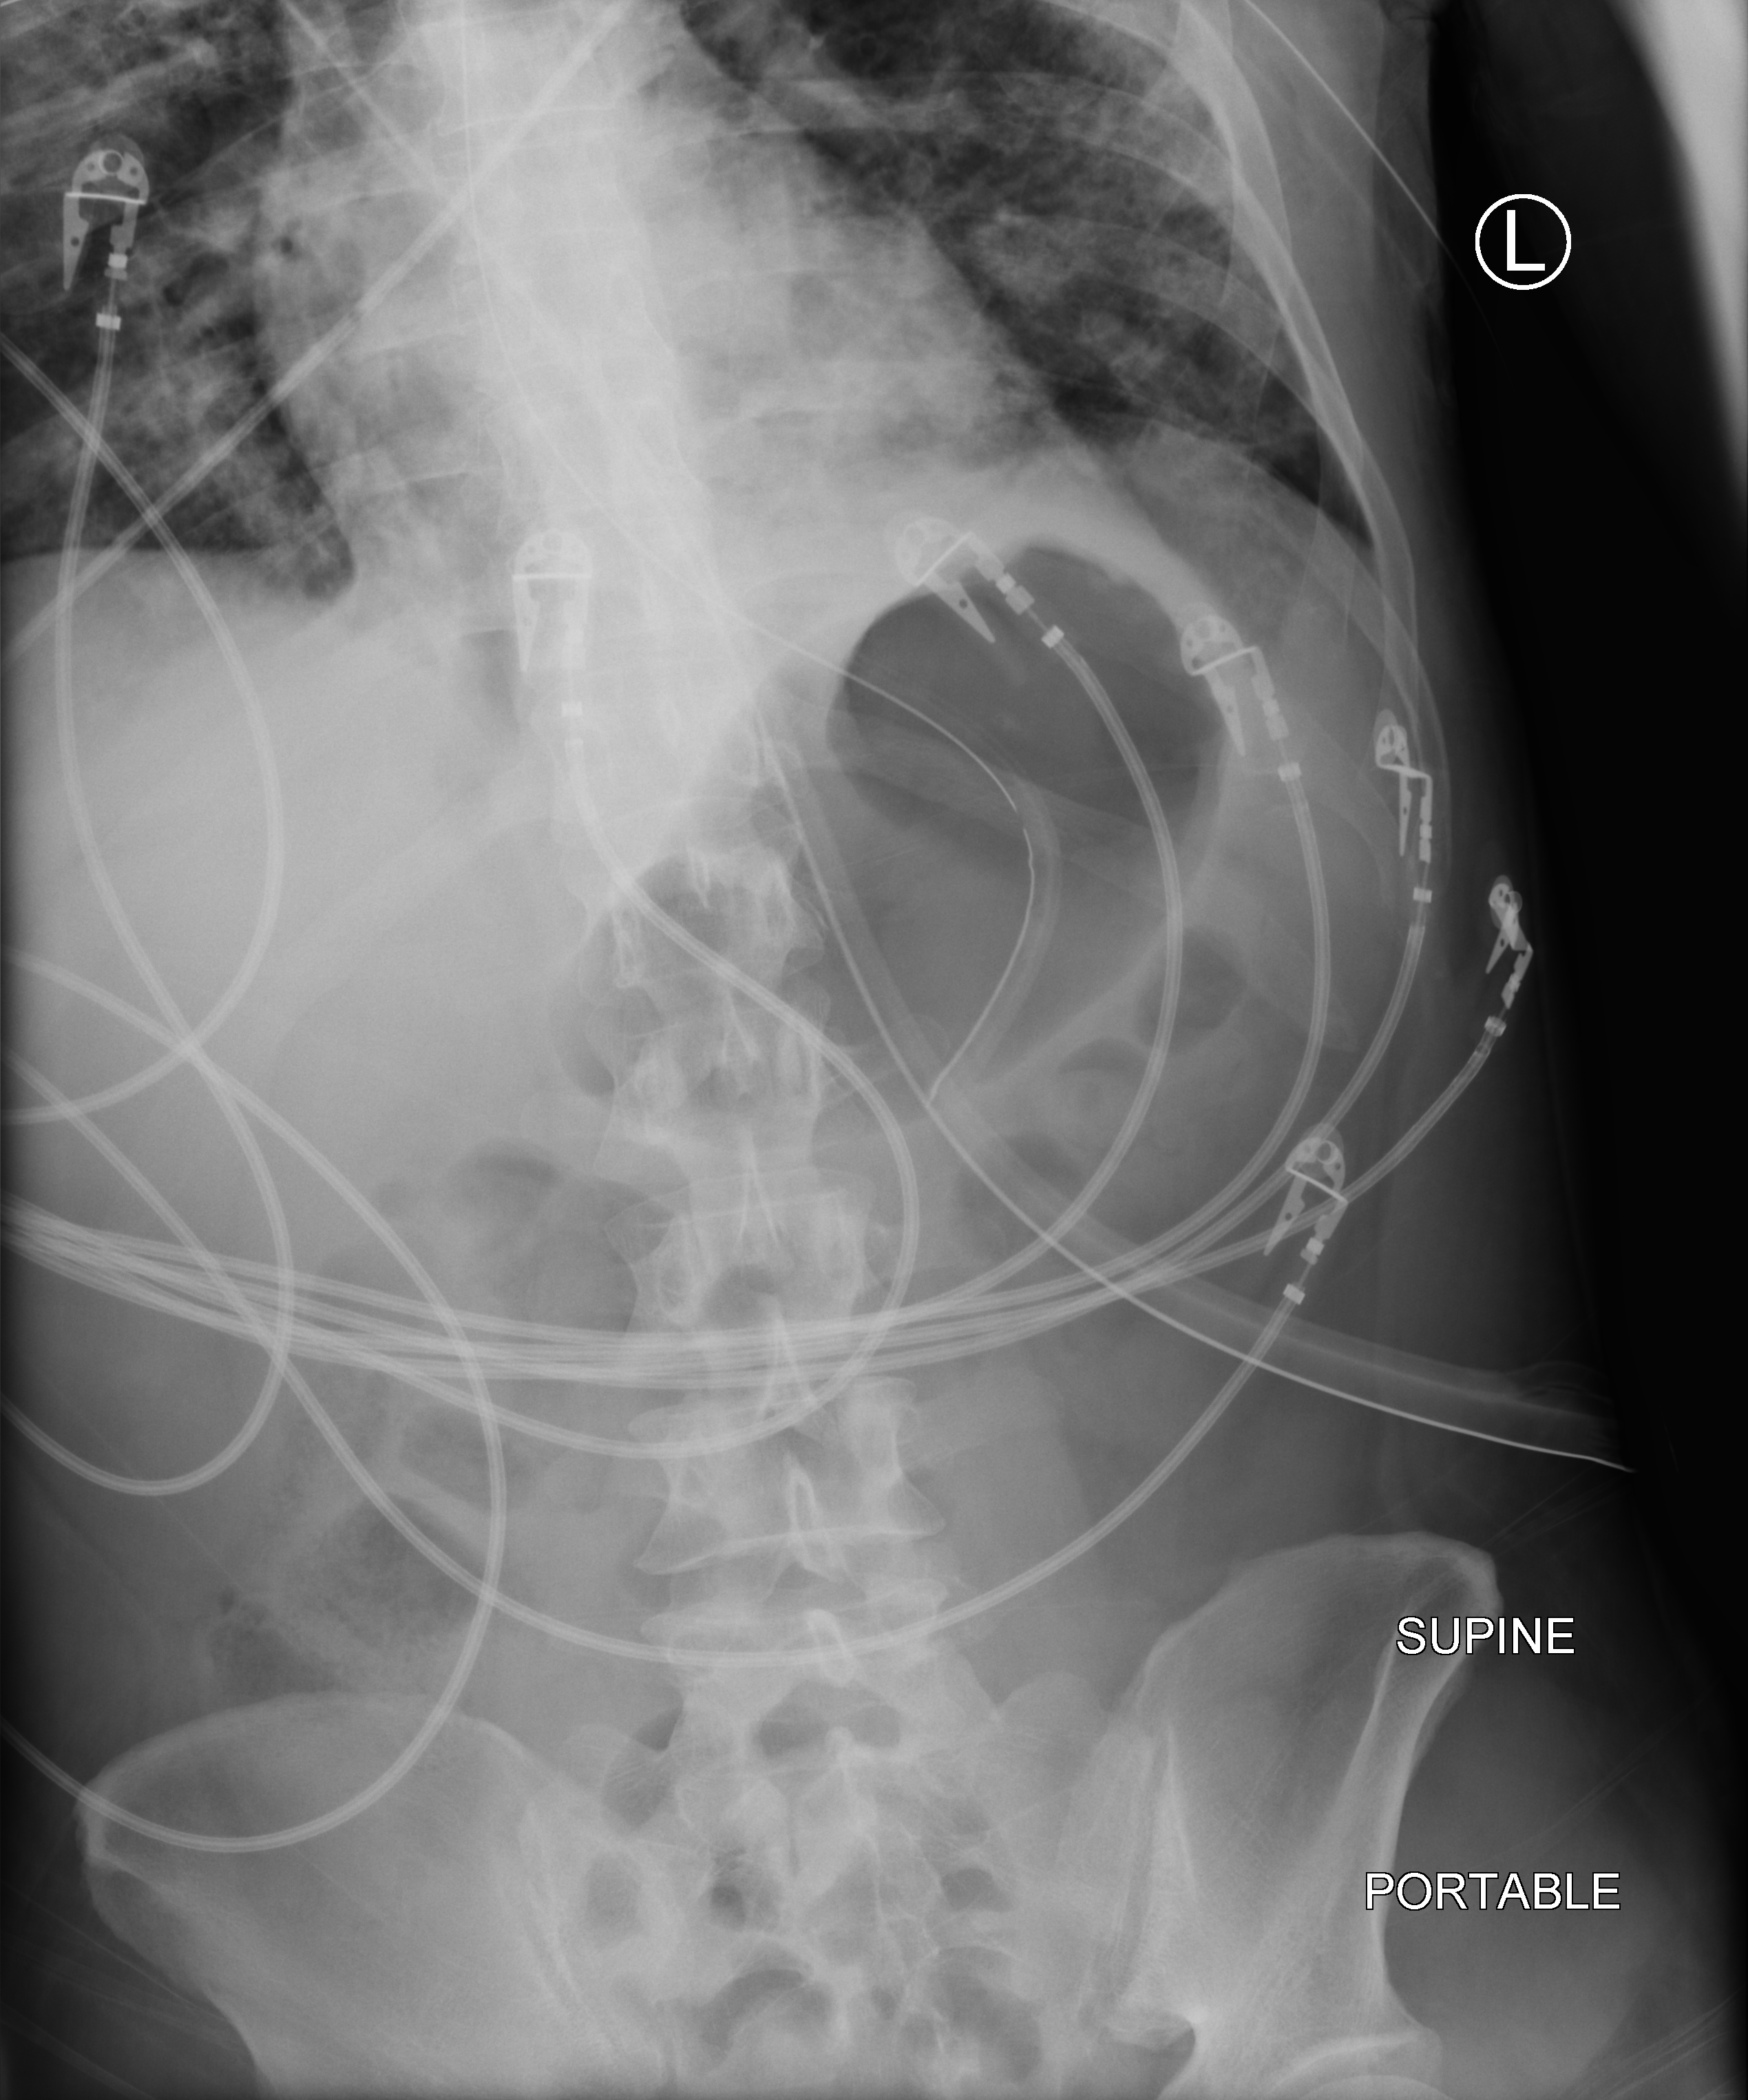
Portable abdomen radiograph; anteroposterior (AP) projection. Patient hospitalised with COVID-19; male, aged 18–59 years.
Admission-level facts for this patient (not findings on this image; timing relative to this image not recorded): mechanically ventilated during this hospital stay: yes.